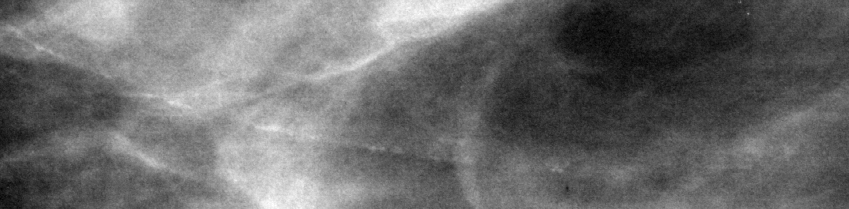
Cropped region of a digitized screen-film mammogram centred on a radiologist-marked abnormality; right breast; MLO view; BI-RADS breast density category 3 (scale 1–4).
Marked abnormality: calcifications, morphology vascular; BI-RADS assessment category 2; benign; no additional work-up was recommended (benign without callback).